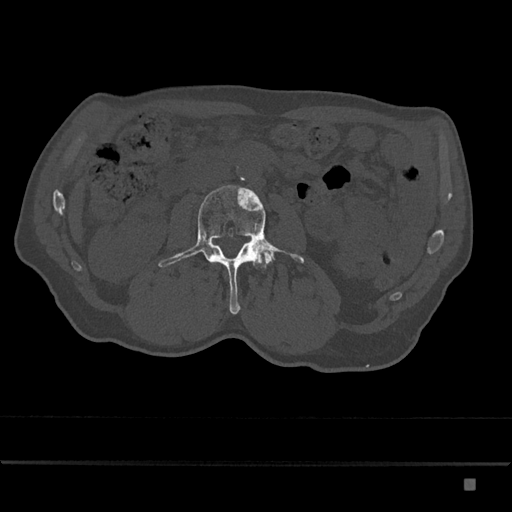
CT including the spine, one axial slice; position 408 of 797 along the scan axis; 120 kVp; bone window (W 1800 / L 400 HU); 512 × 512 image matrix, field of view 390 × 390 mm. Male patient, age 72 years. From the clinical record (not read from this slice): primary cancer: prostate.
Outlined on this slice (semi-automatic segmentation, software-assisted and operator-edited):
- L3 vertebra: bounding box <158,185,304,314> (left, top, right, bottom; pixels)
- L4 vertebra: <261,252,273,268>